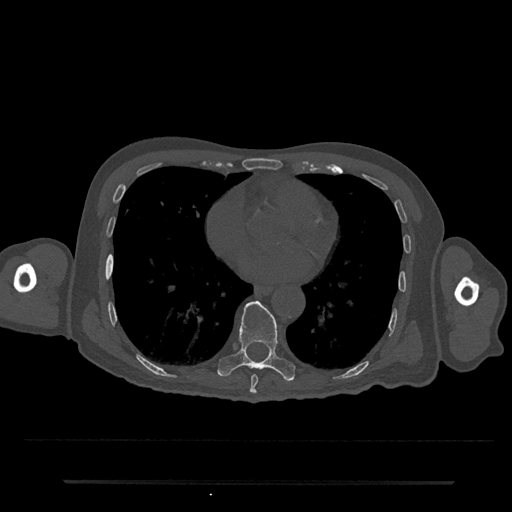
CT including the spine, one axial slice. Position 377 of 797 along the scan axis. Reconstruction kernel Br40s/3. 120 kVp. Bone window (W 1800 / L 400 HU). 0.5 mm slice thickness. 512 × 512 image matrix, field of view 427 × 427 mm. Male patient, age 74 years. Case-level facts recorded for this patient, not image findings: primary cancer: prostate.
Annotated regions visible in this slice (semi-automatically segmented with operator editing):
- T8 vertebra: bounding box <250,375,258,394> (left, top, right, bottom; pixels)
- T9 vertebra: <218,301,295,381>